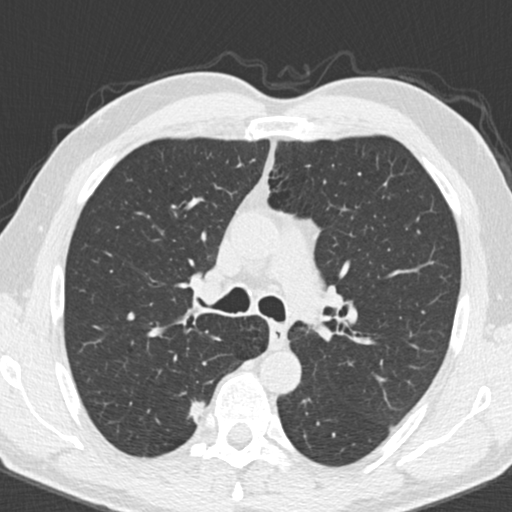
Axial slice from a low-dose chest CT screening exam; third annual screen; lung window (W 1500 / L -600 HU); 2 mm slice thickness. Male, age 55 years at enrolment. Current smoker at enrolment.
- Expert reader's lesion annotation, bounding box <171,394,218,439> (left, top, right, bottom; pixels).
- Screening reader's record for this exam (one nodule recorded; not confirmed to be the boxed lesion): non-calcified nodule or mass ≥4 mm, right upper lobe, 9 × 7 mm, smooth margins, soft tissue attenuation, pre-existing on the prior screen: no.
- Later outcome: lung cancer diagnosed 221 days after this screen — adenocarcinoma, NOS, right upper lobe, poorly differentiated (G3), stage IA (AJCC 6th edition), 15 mm at pathology.